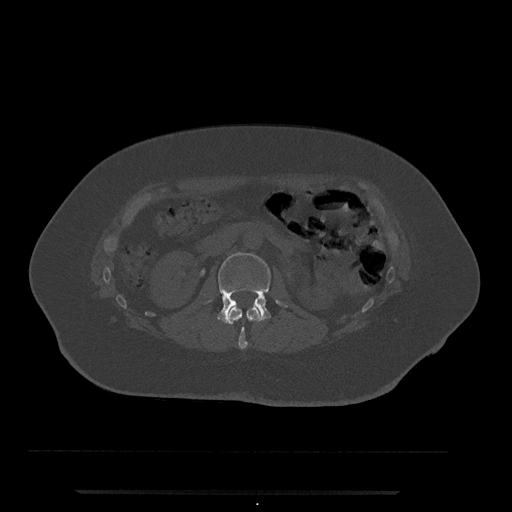
CT including the spine, one axial slice; slice 59 of 797 in the series (ordered by position); reconstruction kernel Br40s/3; 120 kVp; bone window (W 1800 / L 400 HU); 512 × 512 image matrix, field of view 440 × 440 mm. Female patient, age 51 years. Case-level facts recorded for this patient, not image findings: primary cancer: neuro; vertebrae with lytic lesions (as recorded): T8.
Structures marked on this image (semi-automatically segmented with operator editing):
- L1 vertebra: bounding box [x1, y1, x2, y2] px = [226, 307, 262, 349]
- L2 vertebra: [218, 252, 287, 323]